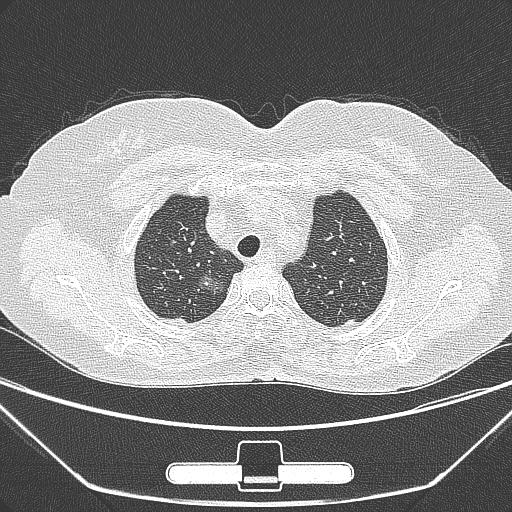
Chest CT, one axial slice; position 231 of 275 along the scan axis; 120 kVp; lung window (W 1500 / L -600 HU); 512 × 512 image matrix. Patient: female, 63 years. Case-level facts recorded for this patient, not image findings: clinical TNM (as recorded): T1a N0 M0.
Outlined on this slice (rectangle marked by the reading radiologist):
- lung tumour (recorded histology: adenocarcinoma): box from (x=195, y=270) to (x=228, y=302) px